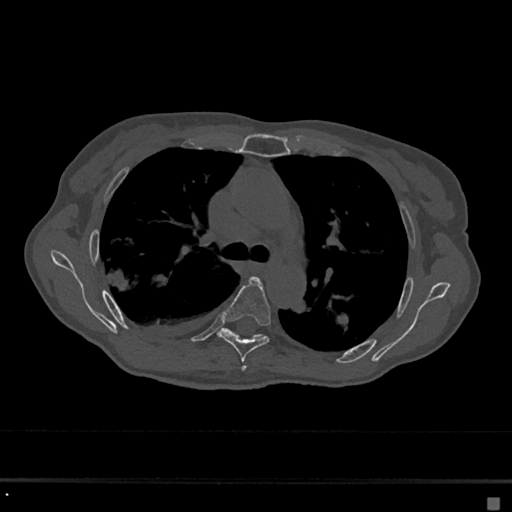
CT including the spine, one axial slice. Slice 455 of 797 in the series (ordered by position). Reconstruction kernel Br40s/3. 120 kVp. Bone window (W 1800 / L 400 HU). 0.5 mm slice thickness. 512 × 512 image matrix. Patient: female, 68 years. Case-level facts recorded for this patient, not image findings: primary cancer: renal.
Outlined on this slice (semi-automatic segmentation, software-assisted and operator-edited):
- T4 vertebra: bounding box (x1, y1, x2, y2) in pixels: (242, 366, 246, 371)
- T5 vertebra: (218, 277, 271, 363)
- T6 vertebra: (222, 328, 265, 339)